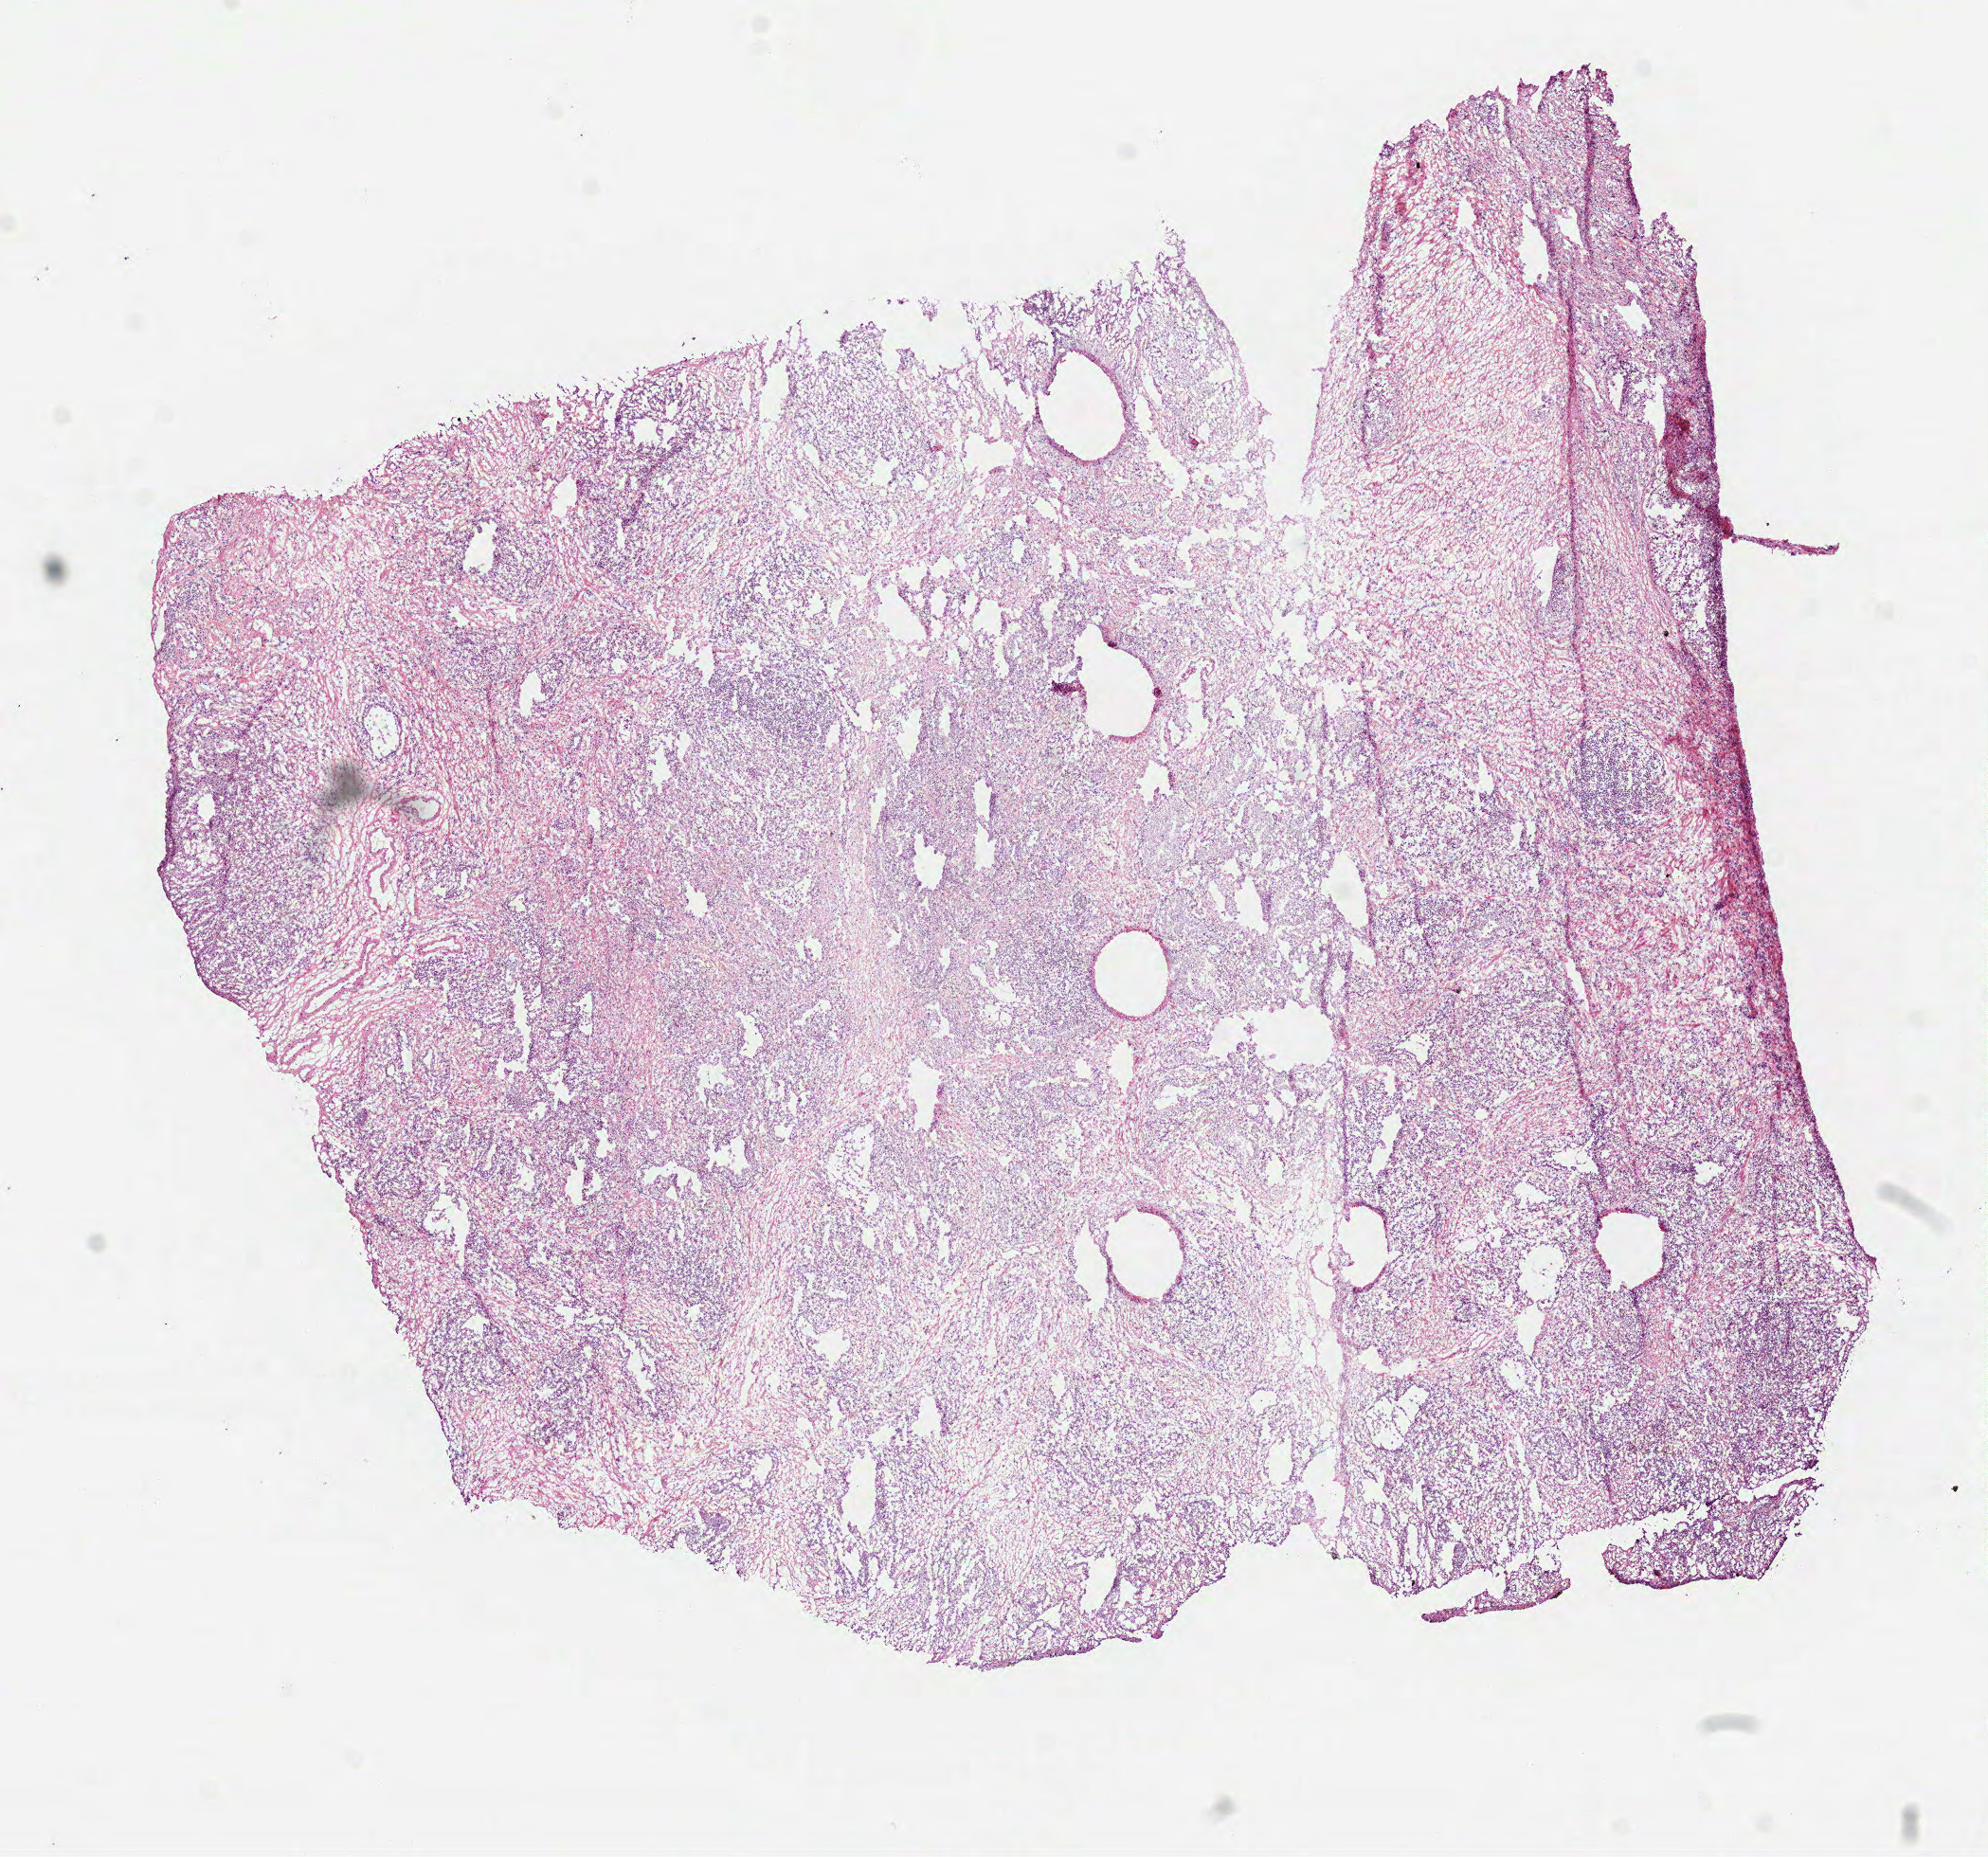
Whole-slide histology image, H&E — low-resolution overview of the scanned area, about 8.5 x 7.9 mm (slide scanned at 40x), frozen section, prostate, primary tumour sample. Male, age 51 years at initial diagnosis. Gleason score: 7 (3+4). Pathologist review of this section (percent, as recorded): tumour cells 90%, tumour nuclei 90%, normal cells 0%, stromal cells 10%, necrosis 0%.
Lymph nodes positive (case pathology): 0 of 4 examined. Pathologic diagnosis: Acinar cell carcinoma (prostate gland). Laterality: bilateral.